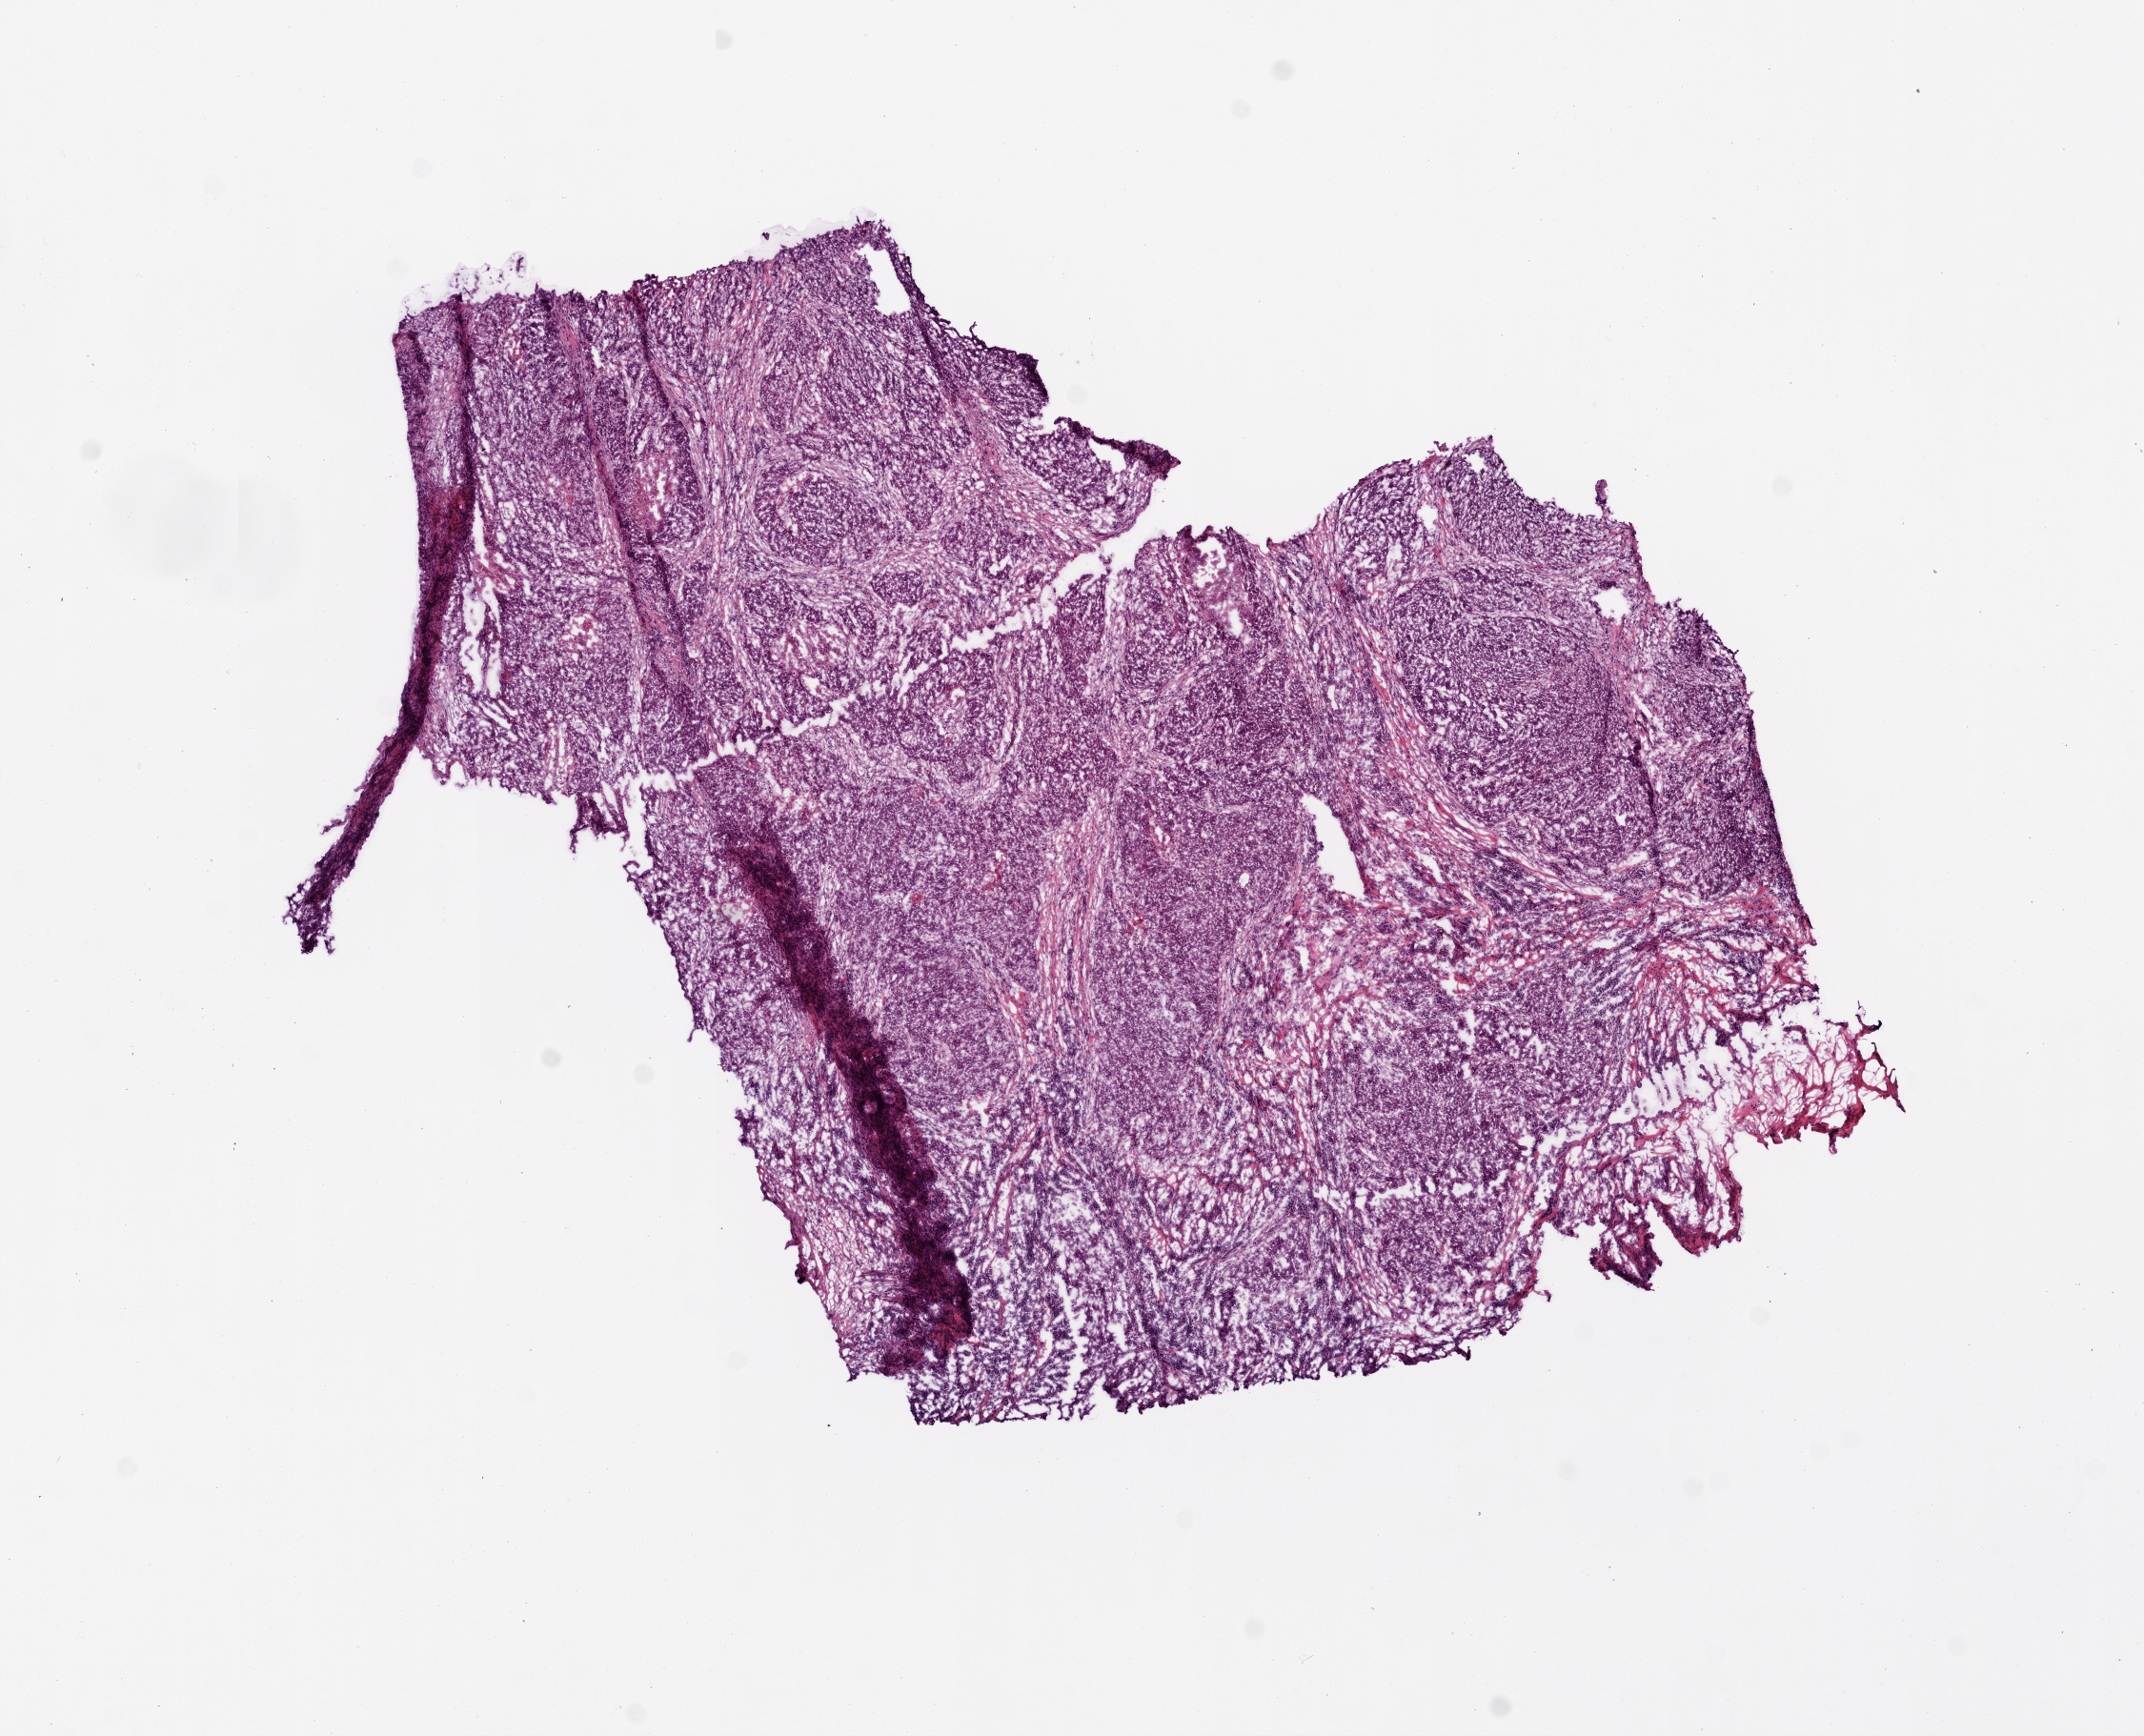
Digitized H&E tissue section (whole slide) — whole scanned area (about 9.0 x 7.3 mm) shown as a low-resolution overview, frozen section from the top of the tissue portion, primary tumour sample from the head and neck. Patient: male, age at initial diagnosis 52 years. Histologic grade: G3 (poorly differentiated). Composition of this section per pathologist review: tumour cells 89%, tumour nuclei 85%, normal cells 0%, stromal cells 10%, necrosis 1%.
- lymph nodes positive (case pathology): 5 of 70 examined
- histologic diagnosis: Squamous cell carcinoma, NOS
- AJCC pathologic stage: IVA (7th edition)
- laterality: left